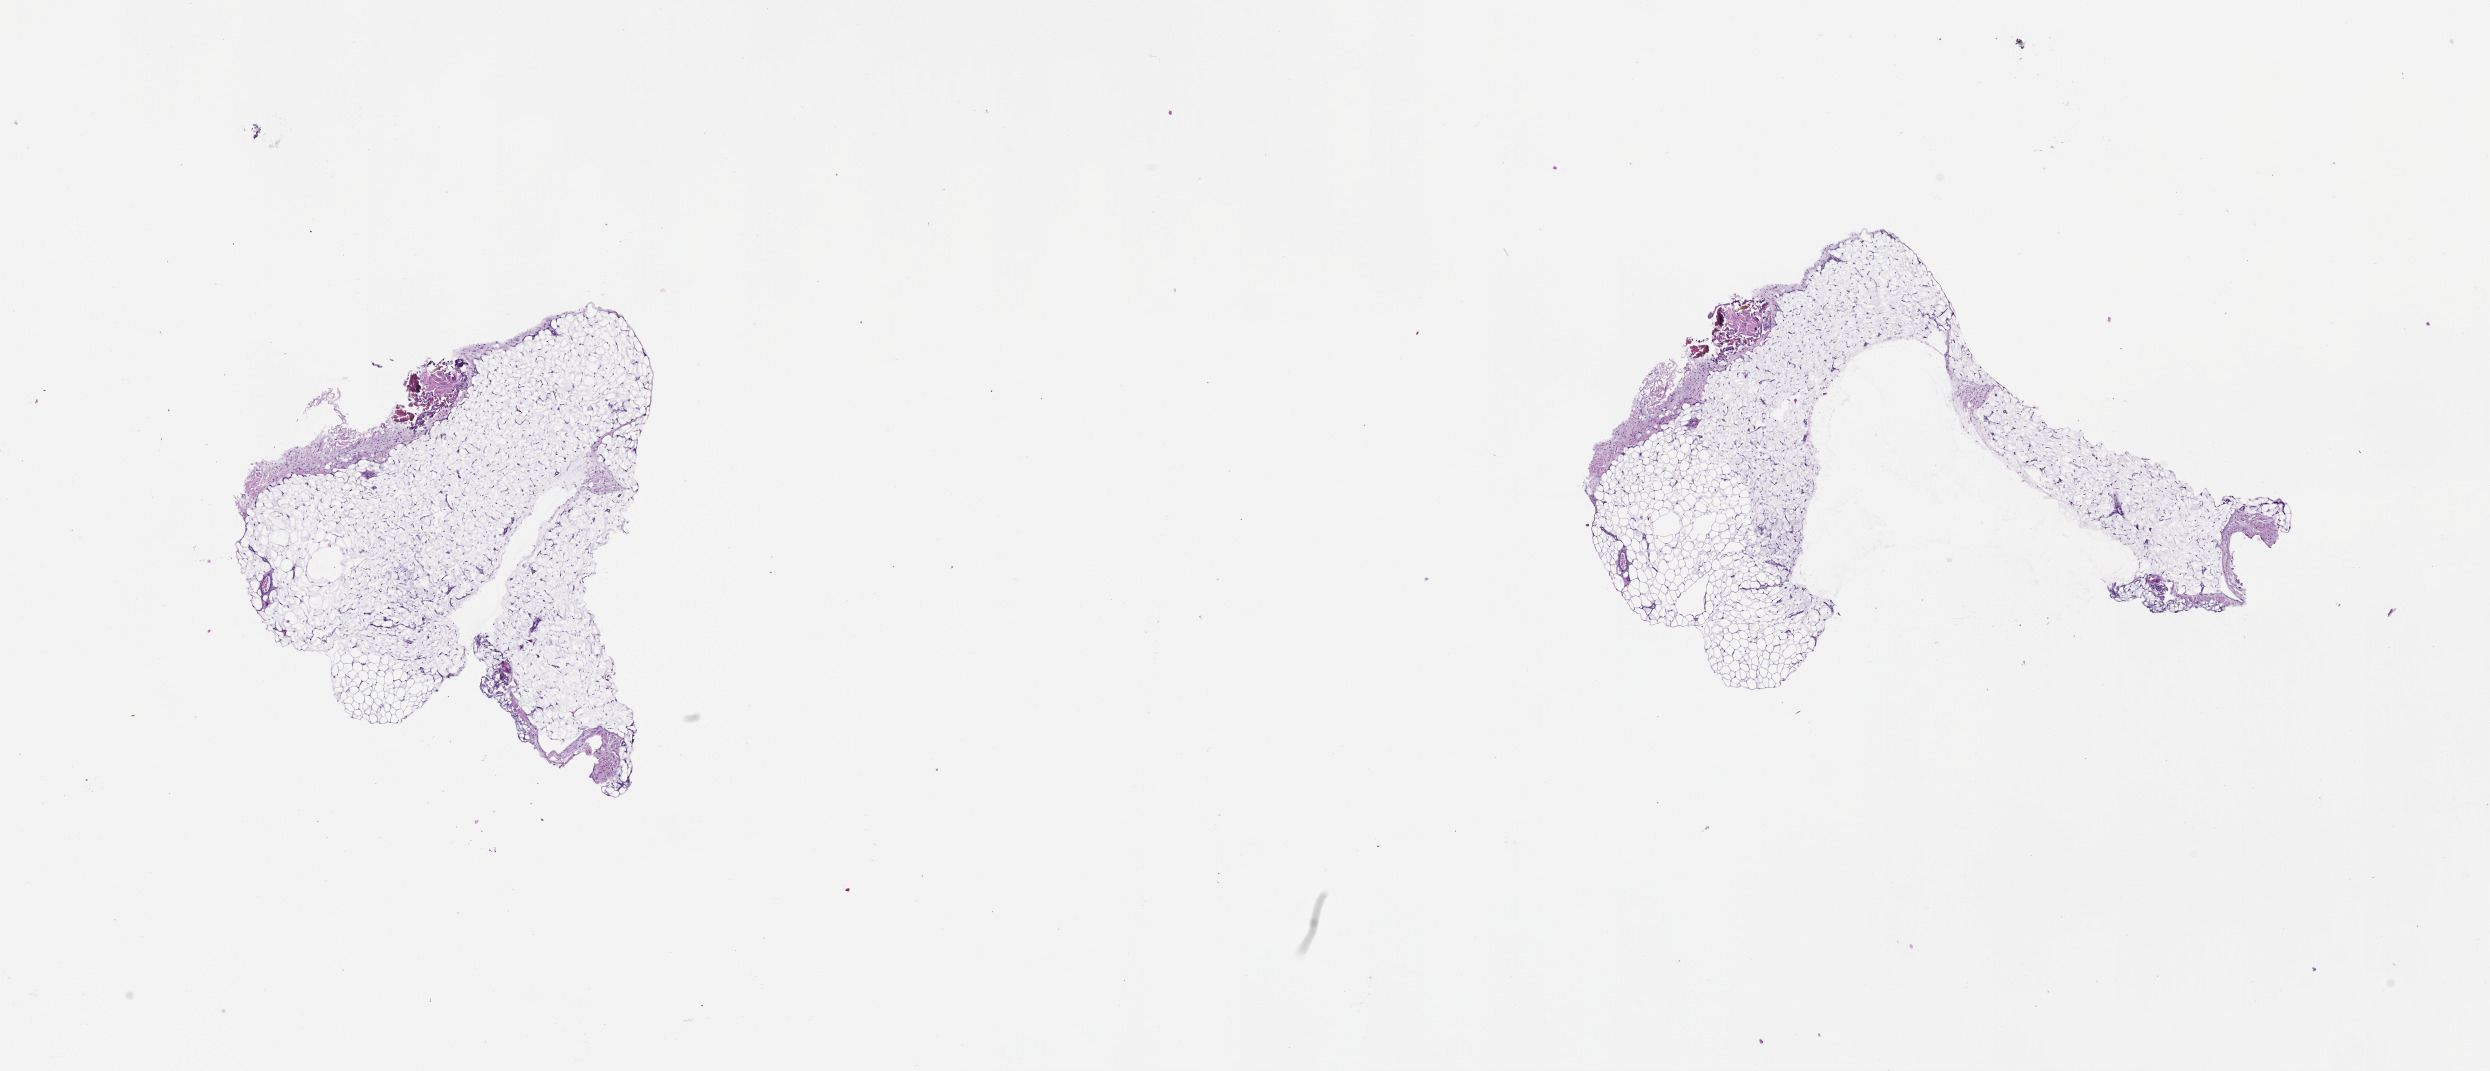
Hematoxylin and eosin (H&E) stained whole-slide image — low-resolution overview of the scanned area, about 20.0 x 8.6 mm (from a 20x scan); normal (non-tumour) tissue sample, sampled site: lymph node. Male, 53 y/o.
- this section: normal (non-tumour) tissue from the same patient
- patient diagnosis: Malignant melanoma, NOS